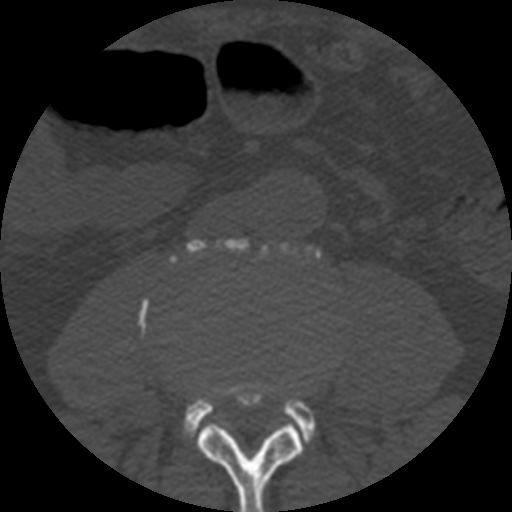
CT including the spine, one axial slice. Position 108 of 508 along the scan axis. 120 kVp. Bone window (W 1800 / L 400 HU). 1.25 mm slice thickness. 512 × 512 image matrix, field of view 160 × 160 mm. Patient age 57 years. Case-level facts recorded for this patient, not image findings: primary cancer: prostate.
Structures marked on this image (semi-automatically segmented with operator editing):
- L3 vertebra: bounding box <197,382,302,512> (left, top, right, bottom; pixels)
- L4 vertebra: <139,238,321,446>